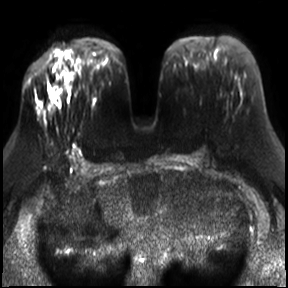
Breast MRI, one axial slice. Diffusion-weighted series; image 2 of 4 stored at this slice position (different b-values; order by instance number). 3 T. 4 mm slice thickness. 288 × 288 image matrix, field of view 340 × 340 mm. Female patient.
Structures marked on this image (outlined manually by an expert reader):
- tumour on diffusion-weighted imaging: box from (x=49, y=87) to (x=55, y=97) px